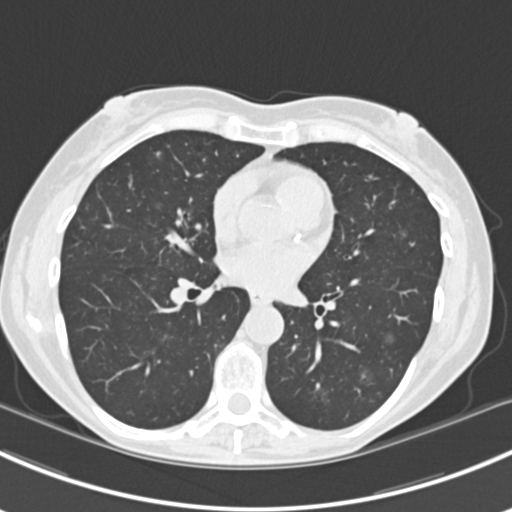
Chest CT (low-dose screening protocol), one axial image. Baseline annual screen. Lung window (W 1500 / L -600 HU). Standard (soft-tissue) reconstruction kernel (B30f). 120 kVp. Slice 99 of 224 in the series. 512 × 512 image matrix, field of view 310 × 310 mm. Female, age 63 years at enrolment. Current smoker at enrolment.
- Expert-annotated lung lesion, bounding box [x1, y1, x2, y2] px = [384, 216, 425, 253].
- The screening reader recorded 10 non-calcified nodules or masses ≥4 mm on this exam (right lower lobe, right lower lobe, left lower lobe, left lower lobe, right middle lobe, right lower lobe, left lower lobe, left upper lobe, right upper lobe, left upper lobe); which of them this box marks is not recorded.
- Later outcome: lung cancer diagnosed 751 days after this screen (after the third annual screen) — bronchiolo-alveolar adenocarcinoma, NOS, right upper lobe, right middle lobe, right lower lobe, left upper lobe, left lower lobe, moderately differentiated (G2), stage IV (AJCC 6th edition).